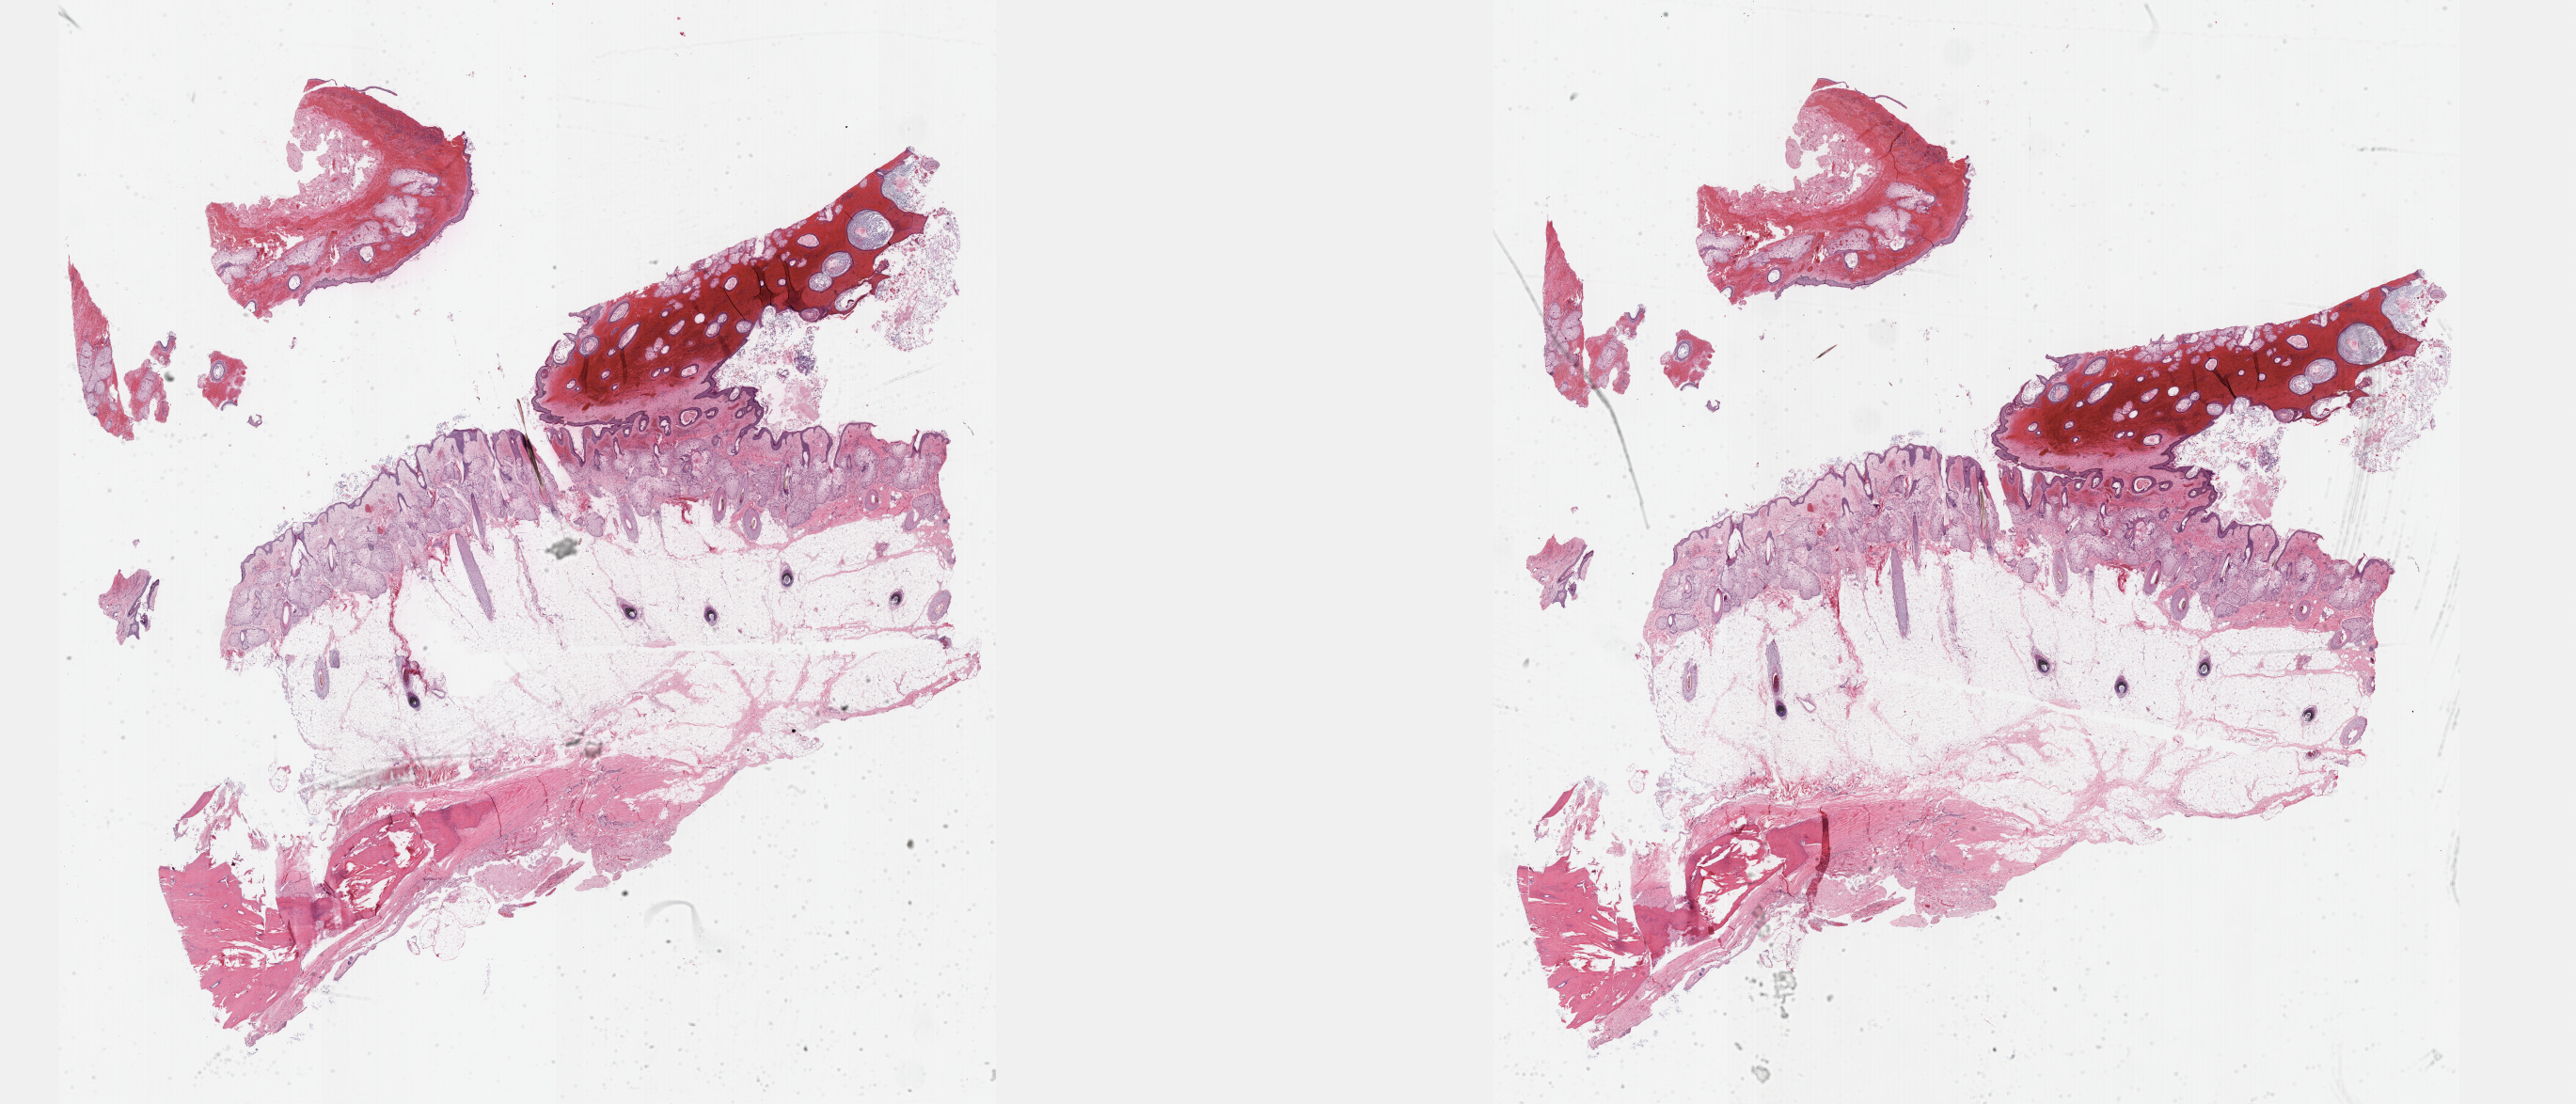
Digitized H&E tissue section (whole slide) — a low-resolution overview of the entire scanned area, about 44.3 x 19.0 mm (from a 40x scan). FFPE section. Sample: primary tumour, kidney. Female patient; age at initial diagnosis 62 years.
Laterality: bilateral. AJCC pathologic stage: I (7th edition). Pathologic diagnosis: Papillary adenocarcinoma, NOS.